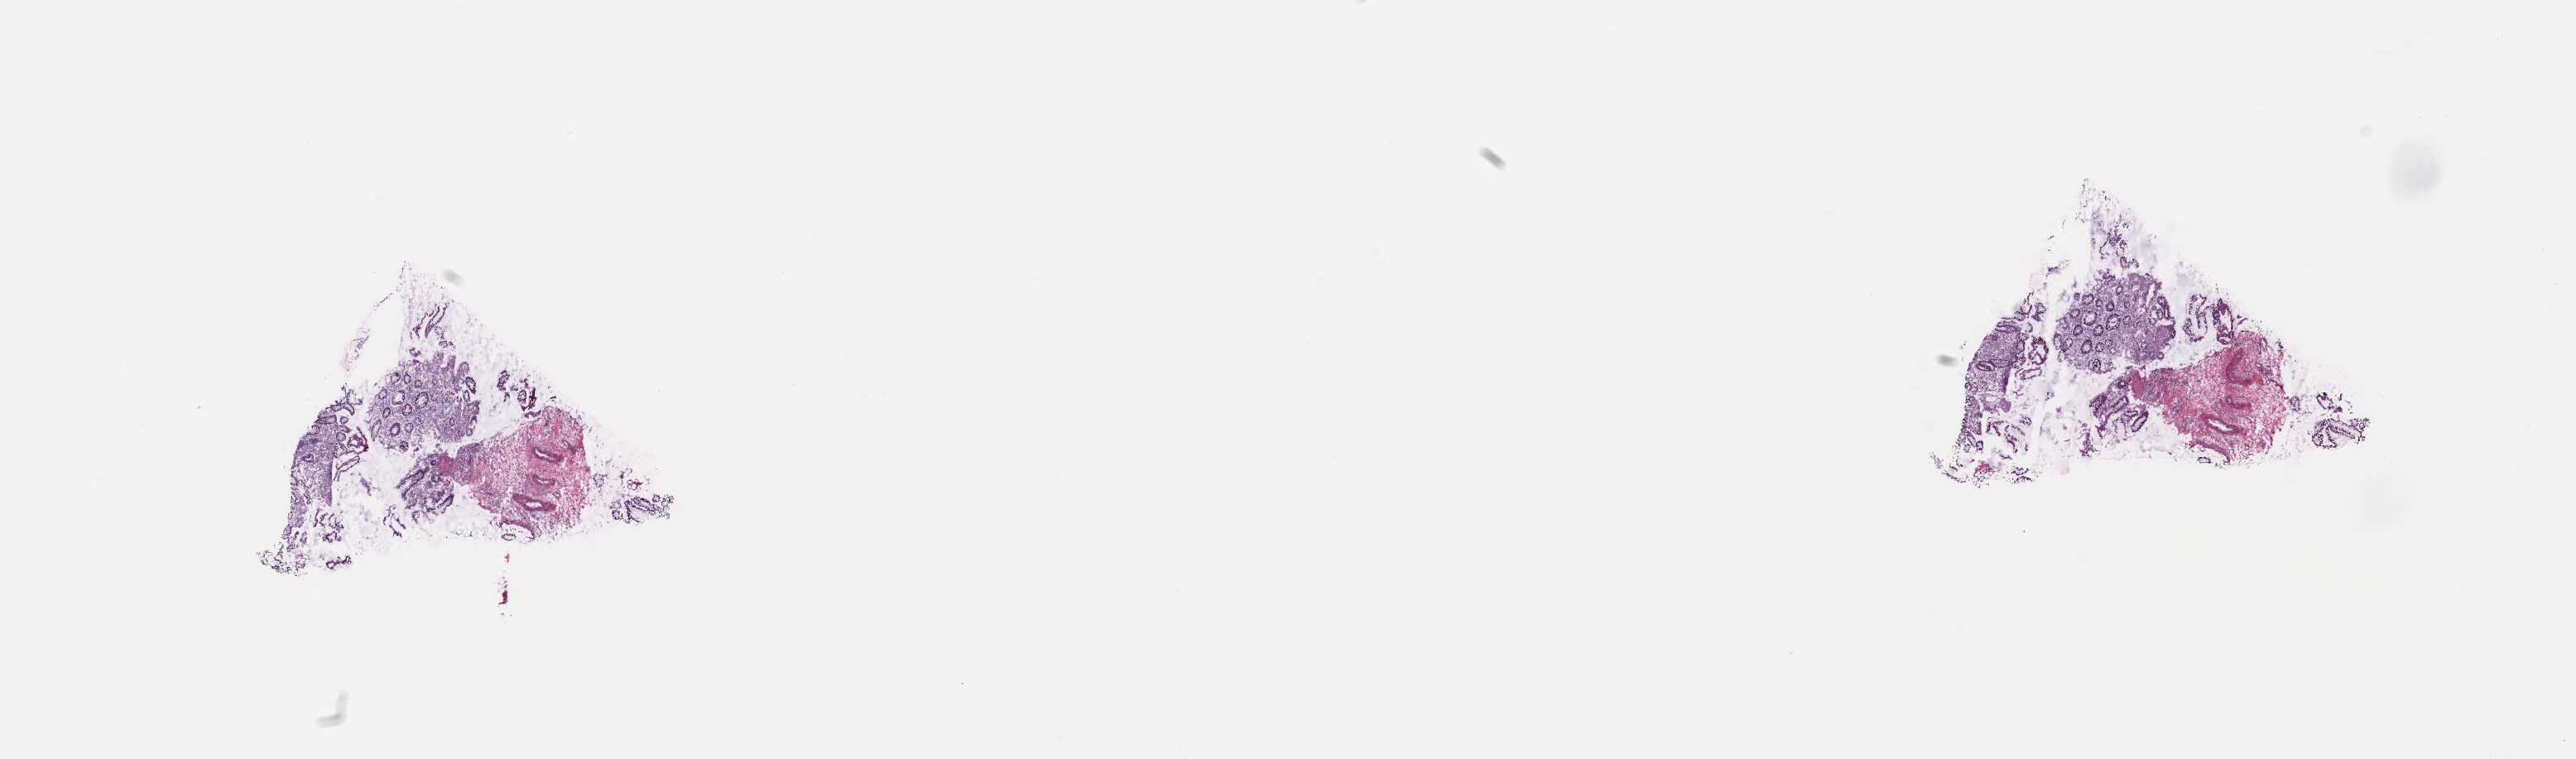
Haematoxylin and eosin whole-slide image, low-resolution overview of the scanned area, about 25.1 x 7.4 mm, frozen section, specimen: normal-tissue sample (non-tumor) from a patient with adenocarcinoma, NOS, anatomic site: splenic flexure of colon. Patient sex: female. Composition of this section per pathologist review: tumor cells 0%, tumor nuclei 0%, stromal cells 65%, necrosis 0%, normal cells 35%. Inflammatory infiltration, as recorded: lymphocyte infiltration 80%, monocyte infiltration 1%, neutrophil infiltration 0%.
This section: non-tumor tissue sample; the patient's diagnosis is given above. Section: bottom of the tissue portion.